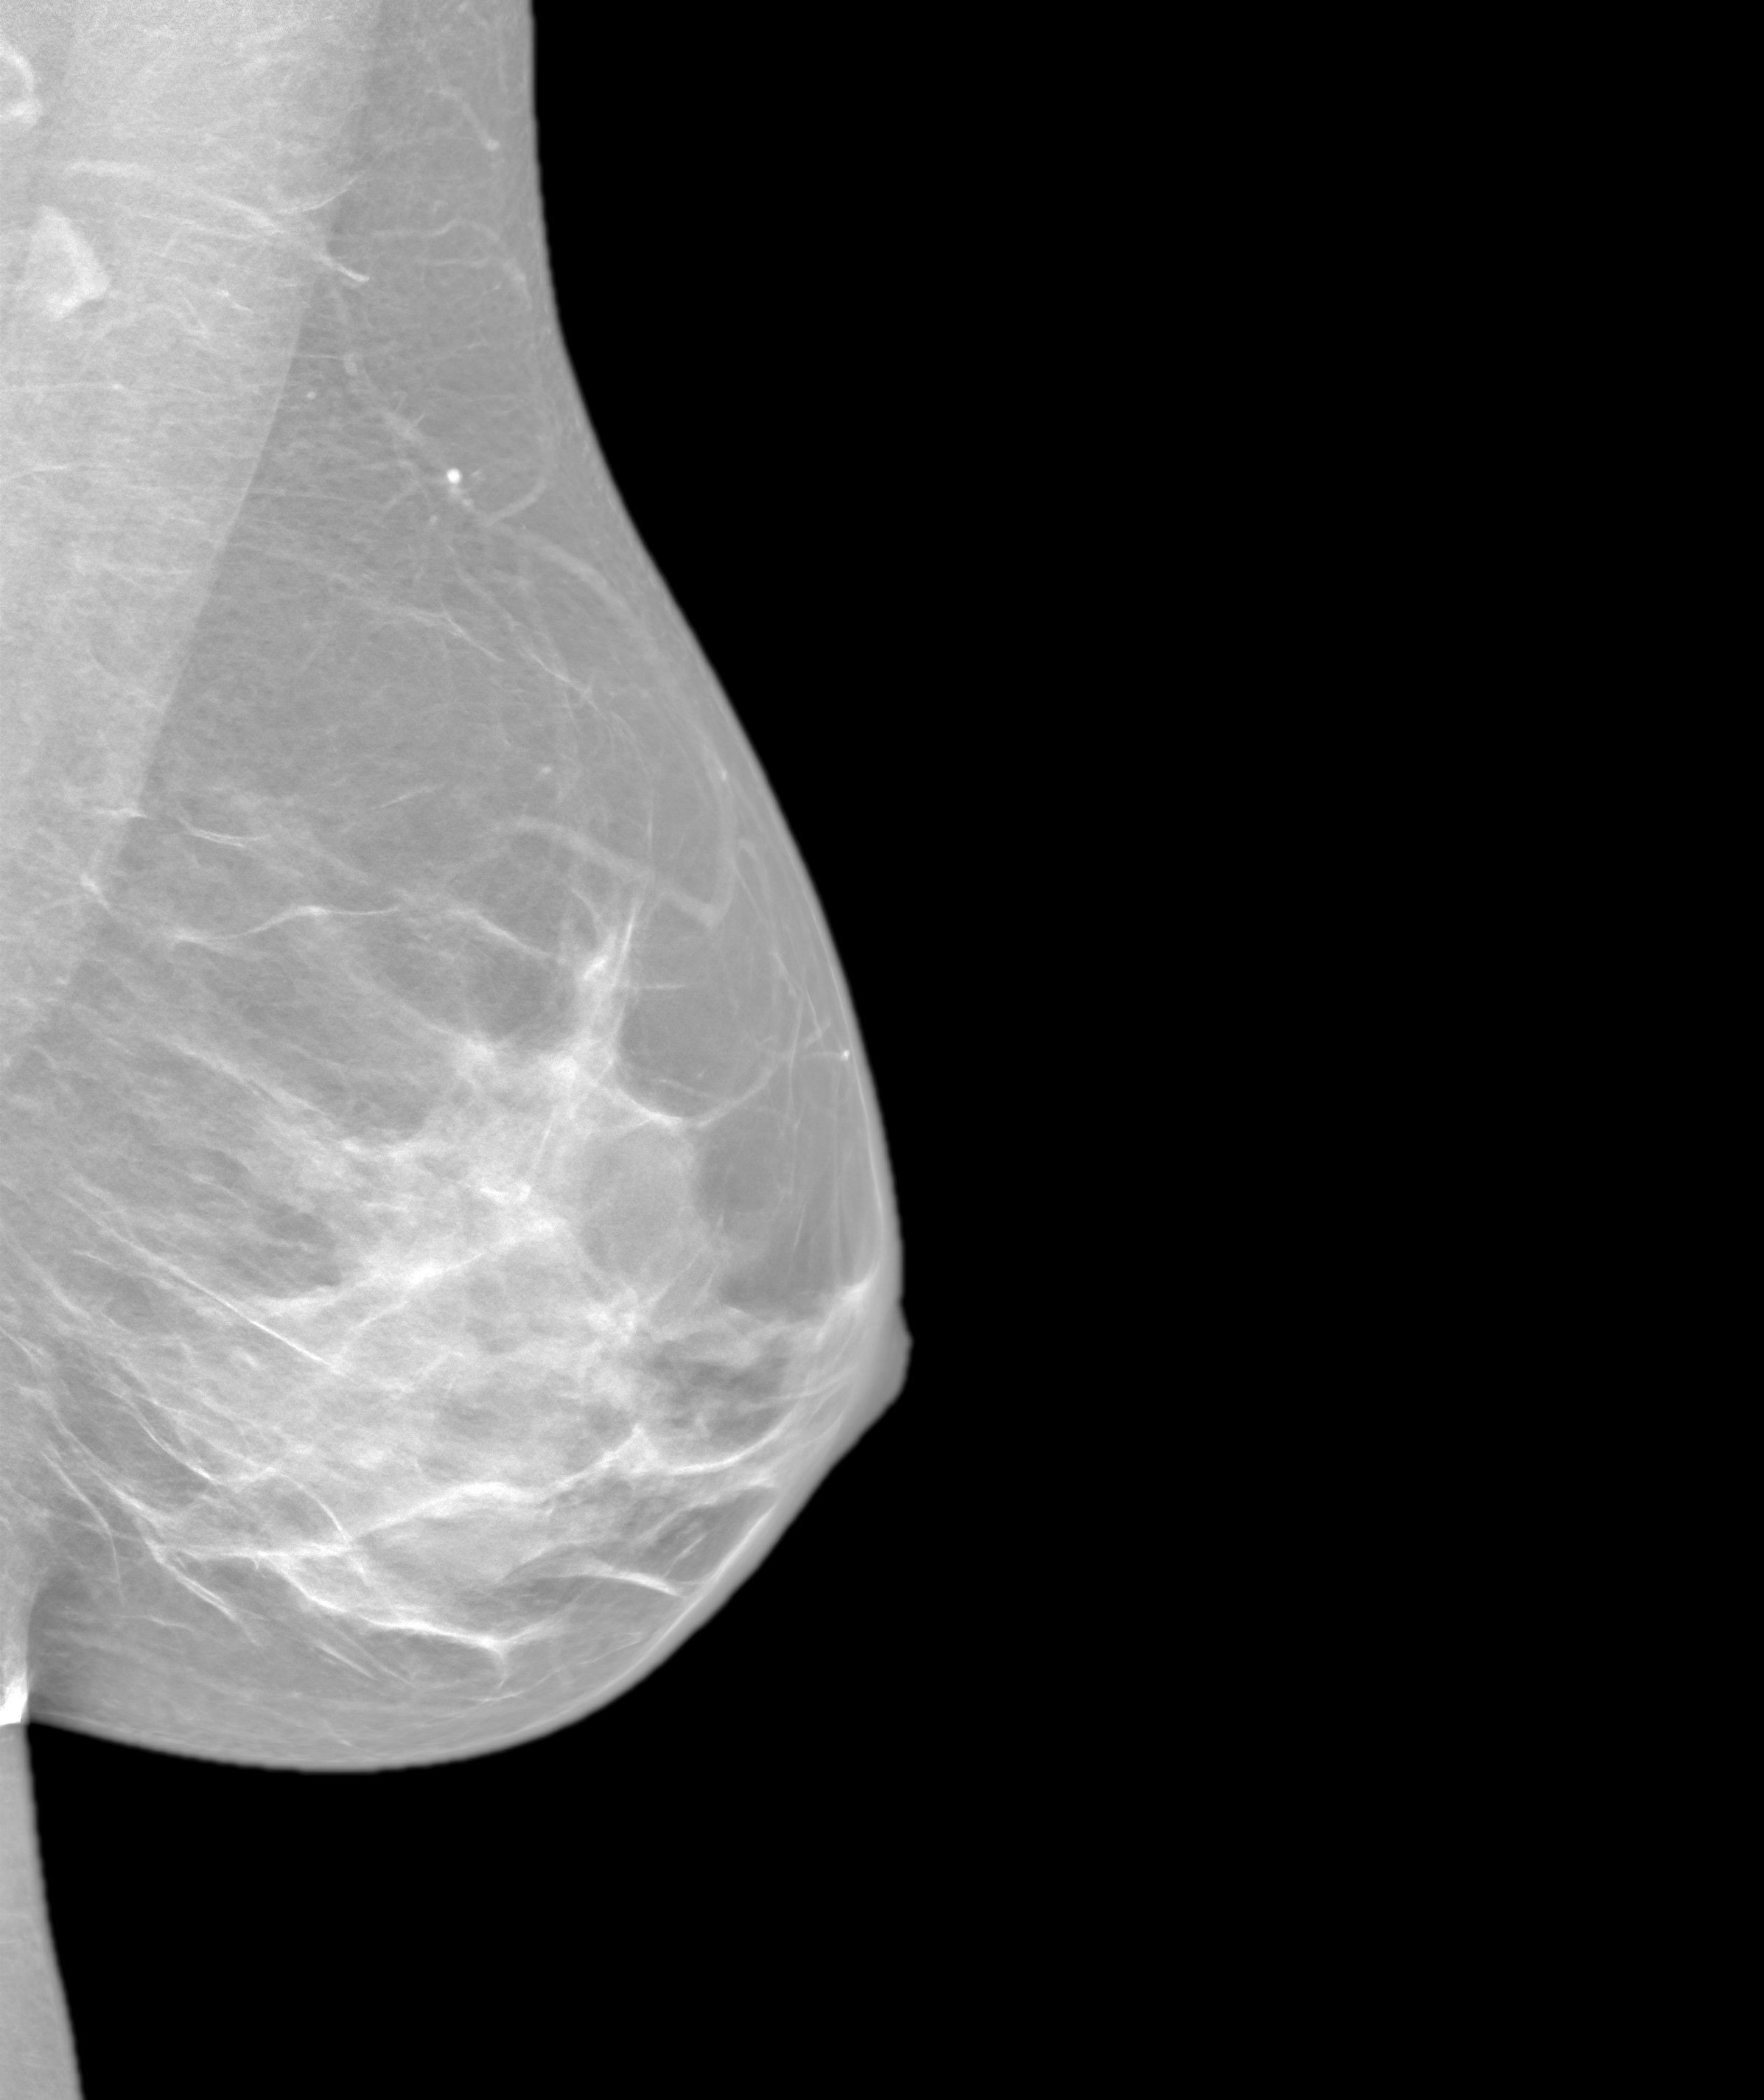
Screening examination. Female patient, age 45 years.
Image type: synthesized 2-D view from tomosynthesis. Breast: left. Projection: medio-lateral oblique projection.